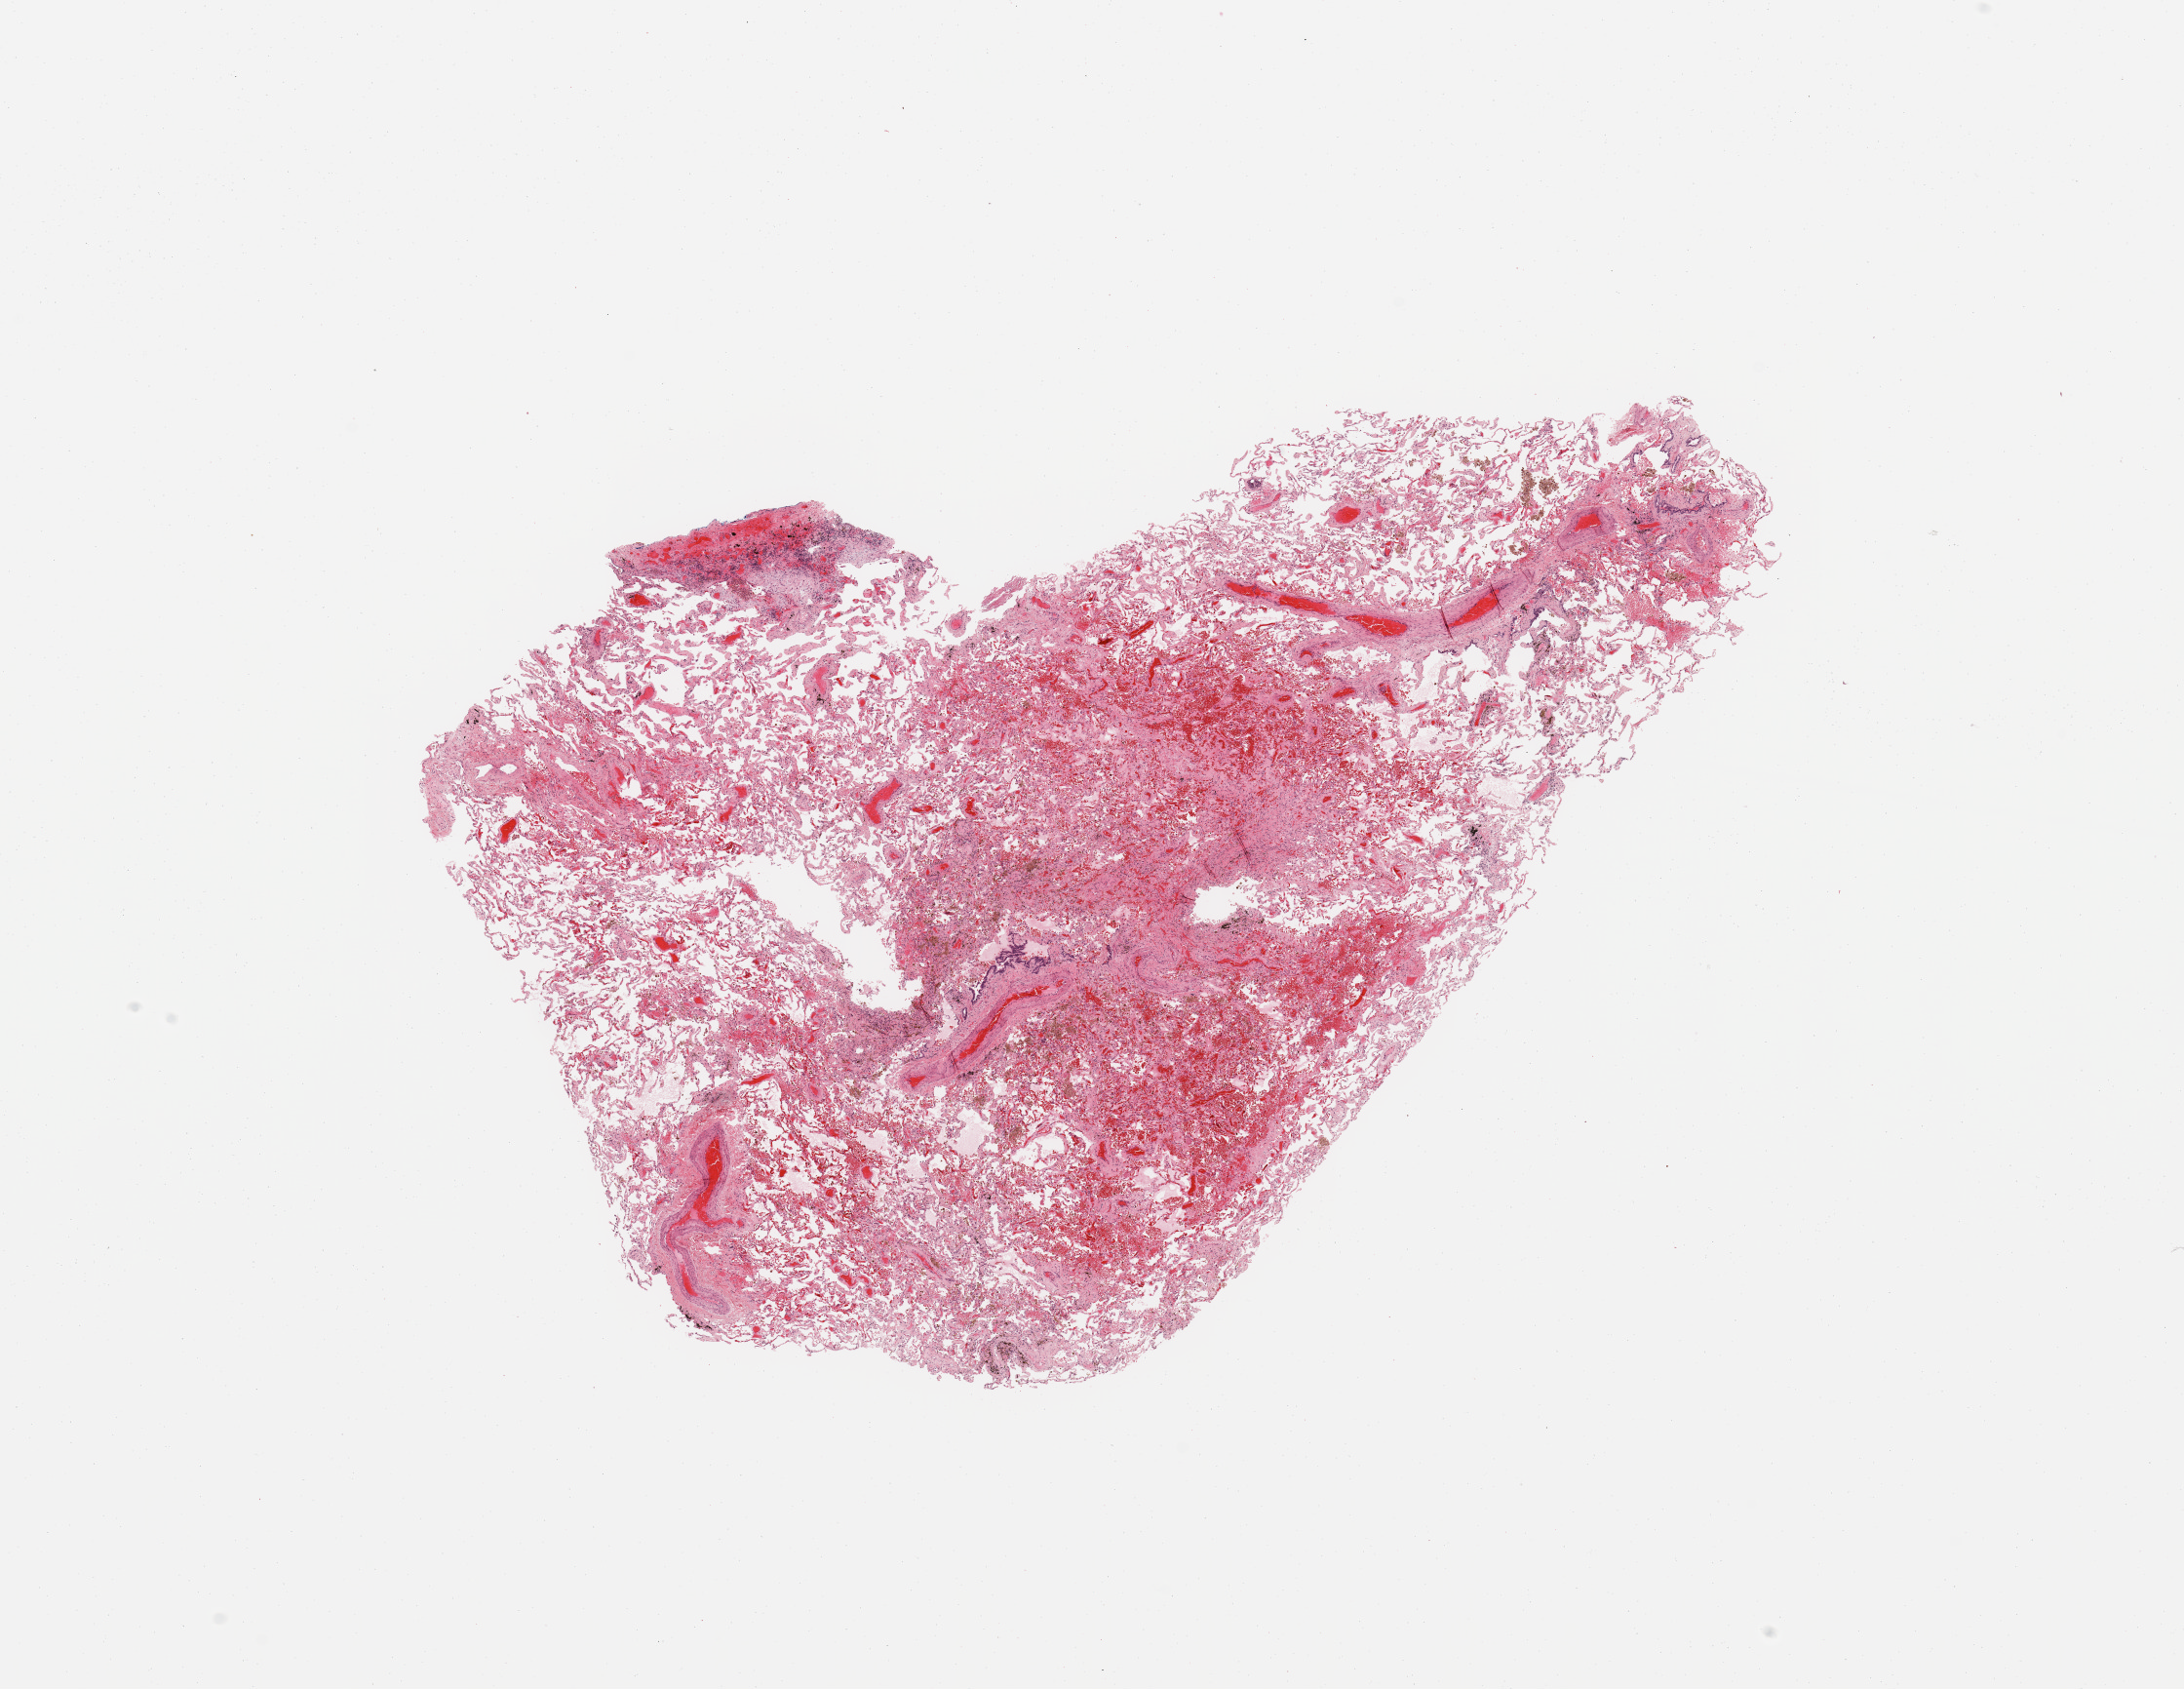
Whole-slide histology image, Hematoxylin and eosin (H&E) stained, whole scanned area (about 17.7 x 13.7 mm, from a 20x scan) shown as a low-resolution overview. Normal (non-tumour) tissue sample, sampled site: lung. 66-year-old male patient.
This section: normal (non-tumour) tissue from the same patient. Patient diagnosis: Adenocarcinoma, NOS.